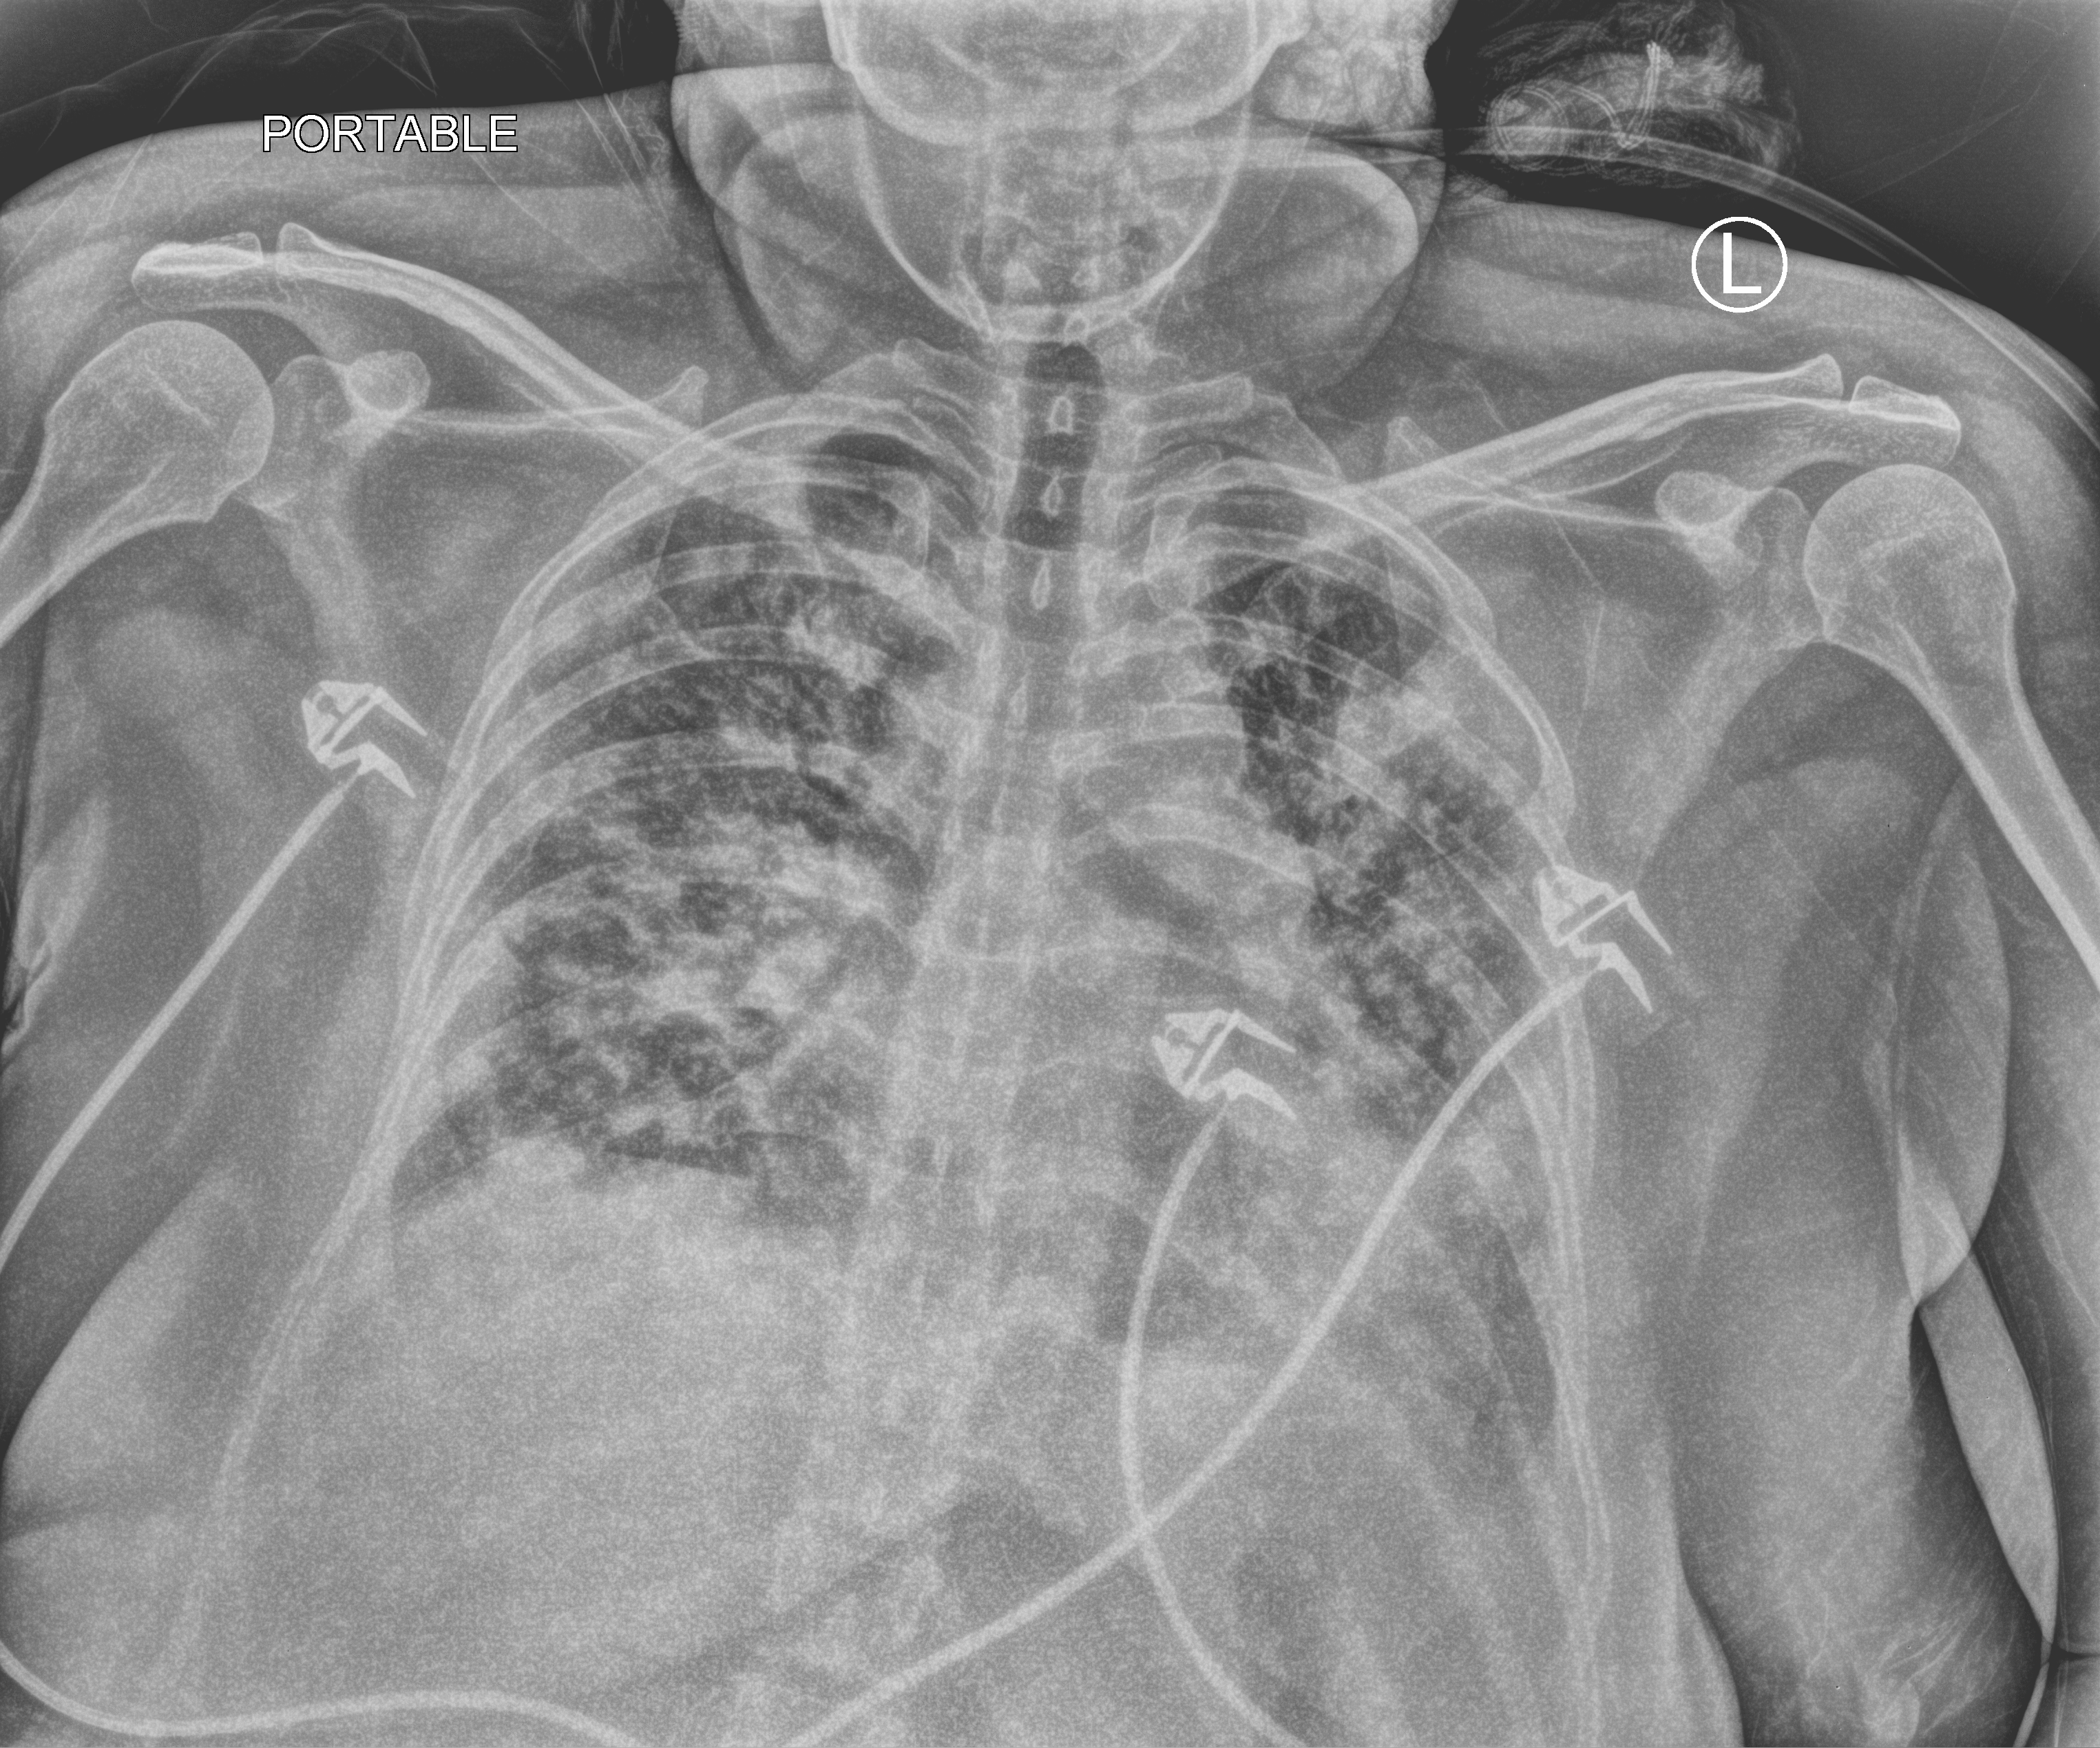
Portable chest radiograph; anteroposterior (AP) projection. Adult patient hospitalised with COVID-19, age 18–59 years.
Hospital-stay facts (about this admission, not read from this image; timing relative to this image not recorded): mechanically ventilated during this hospital stay: yes.